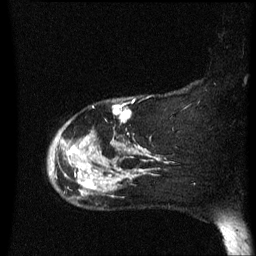
Breast MRI (dynamic contrast-enhanced), one sagittal slice. Position 53 of 60 along the scan axis. Dynamic contrast-enhanced series, image 2 of 3 at this slice position (ordered by acquisition). 1.5 T. TE 4.2 ms, TR 8.4 ms. 256 × 256 image matrix. Female patient, age 47 years.
Outlined on this slice (semi-automatically segmented with operator editing):
- analysis volume of interest (the breast-tissue region the enhancement analysis was run in; not a lesion): bounding box (x1, y1, x2, y2) in pixels: (48, 107, 149, 206)
- tumour enhancement mask (voxels above the 70 % enhancement threshold inside the analysis volume of interest): (66, 107, 141, 191)